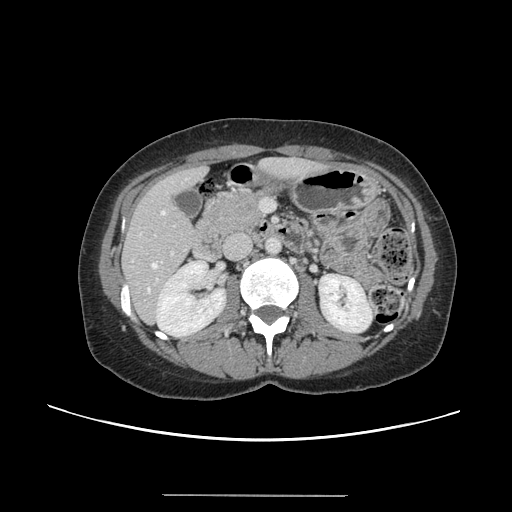
Contrast-enhanced abdominal CT, one axial slice; slice 58 of 144 in the series (ordered by position); 120 kVp; intravenous contrast given; soft-tissue window (W 400 / L 40 HU); 2.5 mm slice thickness; 512 × 512 image matrix, field of view 380 × 380 mm. Female patient, age 53 years. Case-level facts recorded for this patient, not image findings: diagnosis: colorectal cancer liver metastases, imaged before liver resection; multiple liver metastases: yes; largest metastasis: 1.1 cm; disease in both lobes: no.
Outlined on this slice (outlined manually by an expert reader):
- hepatic veins: box from (x=148, y=211) to (x=165, y=291) px
- liver: (x=124, y=159)–(x=321, y=321)
- planned liver remnant (the part of the liver to remain after resection): (x=124, y=159)–(x=322, y=310)
- portal vein (with intrahepatic branches): (x=156, y=252)–(x=174, y=282)